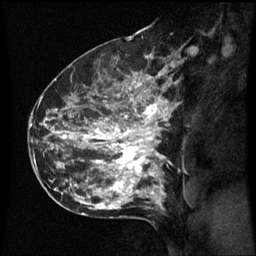
Breast MRI (dynamic contrast-enhanced), one sagittal slice; slice 39 of 60 in the series (ordered by position); dynamic contrast-enhanced series, image 2 of 3 at this slice position (ordered by acquisition); 1.5 T; TE 4.2 ms, TR 8.9 ms; 2.1 mm slice thickness; 256 × 256 image matrix, field of view 200 × 200 mm. Patient: female, 42 years. From the clinical record (not read from this slice): setting: breast cancer imaged before/during neoadjuvant chemotherapy; receptor status: HER2-positive.
Structures marked on this image (semi-automatic segmentation, software-assisted and operator-edited):
- analysis volume of interest (the breast-tissue region the enhancement analysis was run in; not a lesion): bounding box (x1, y1, x2, y2) in pixels: (66, 82, 171, 193)
- tumour enhancement mask (voxels above the 70 % enhancement threshold inside the analysis volume of interest): (68, 82, 167, 193)